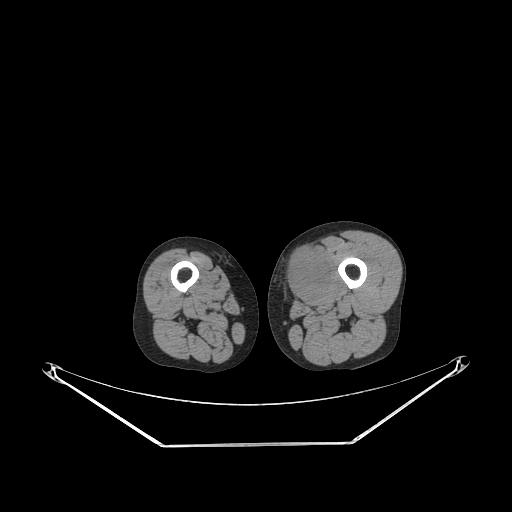
CT of an extremity soft-tissue mass (from a PET/CT study), one axial slice; position 219 of 267 along the scan axis; reconstruction kernel STANDARD; soft-tissue window (W 400 / L 40 HU); 3.75 mm slice thickness; 512 × 512 image matrix, field of view 500 × 500 mm. Male patient. Case-level facts recorded for this patient, not image findings: histological type: pleiomorphic leiomyosarcoma; grade: high; site of the primary tumour: left thigh.
Structures marked on this image (expert contour drawn on MRI and transferred to this co-registered scan by the dataset authors):
- gross tumour volume including surrounding oedema: bounding box <283,249,330,300> (left, top, right, bottom; pixels)
- gross tumour volume (mass): <283,249,325,300>